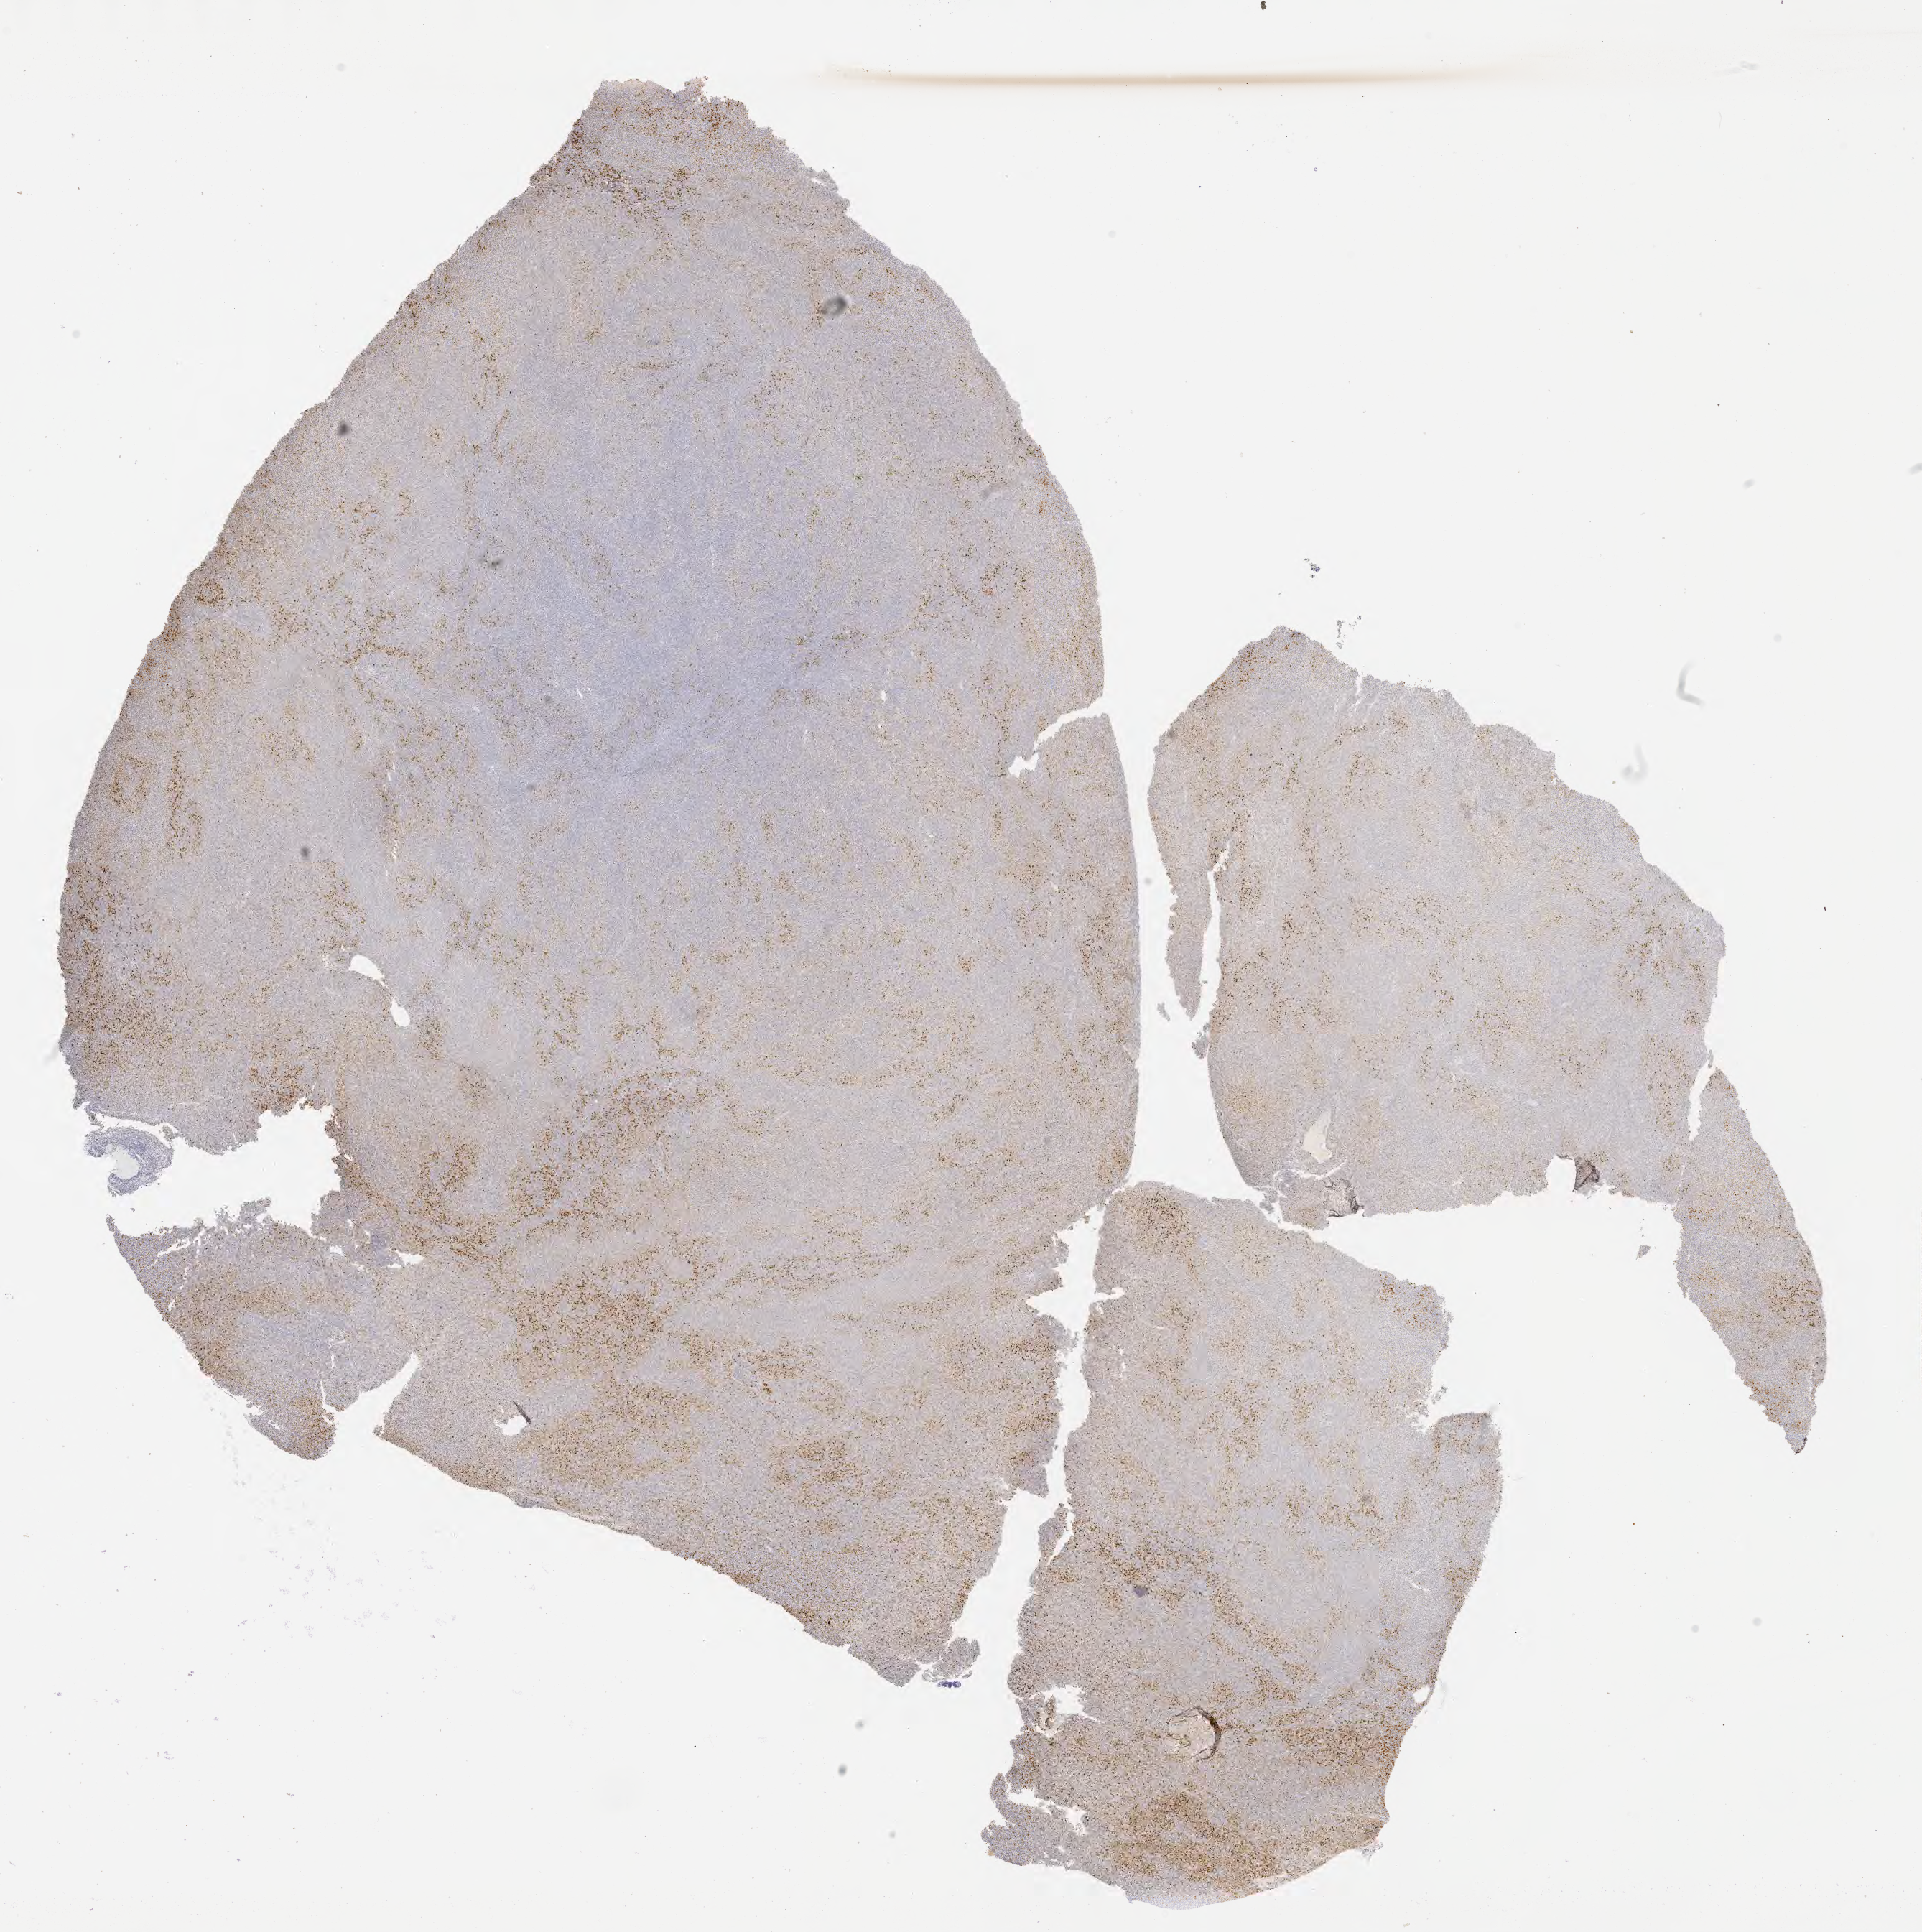
Immunohistochemistry (IHC) whole-slide image stained for BCL6 — low-resolution overview of the scanned area, about 21.6 x 21.7 mm, tumor tissue, site: liver. Patient: female, age 46 years.
• histologic diagnosis: Diffuse large B-cell lymphoma, NOS